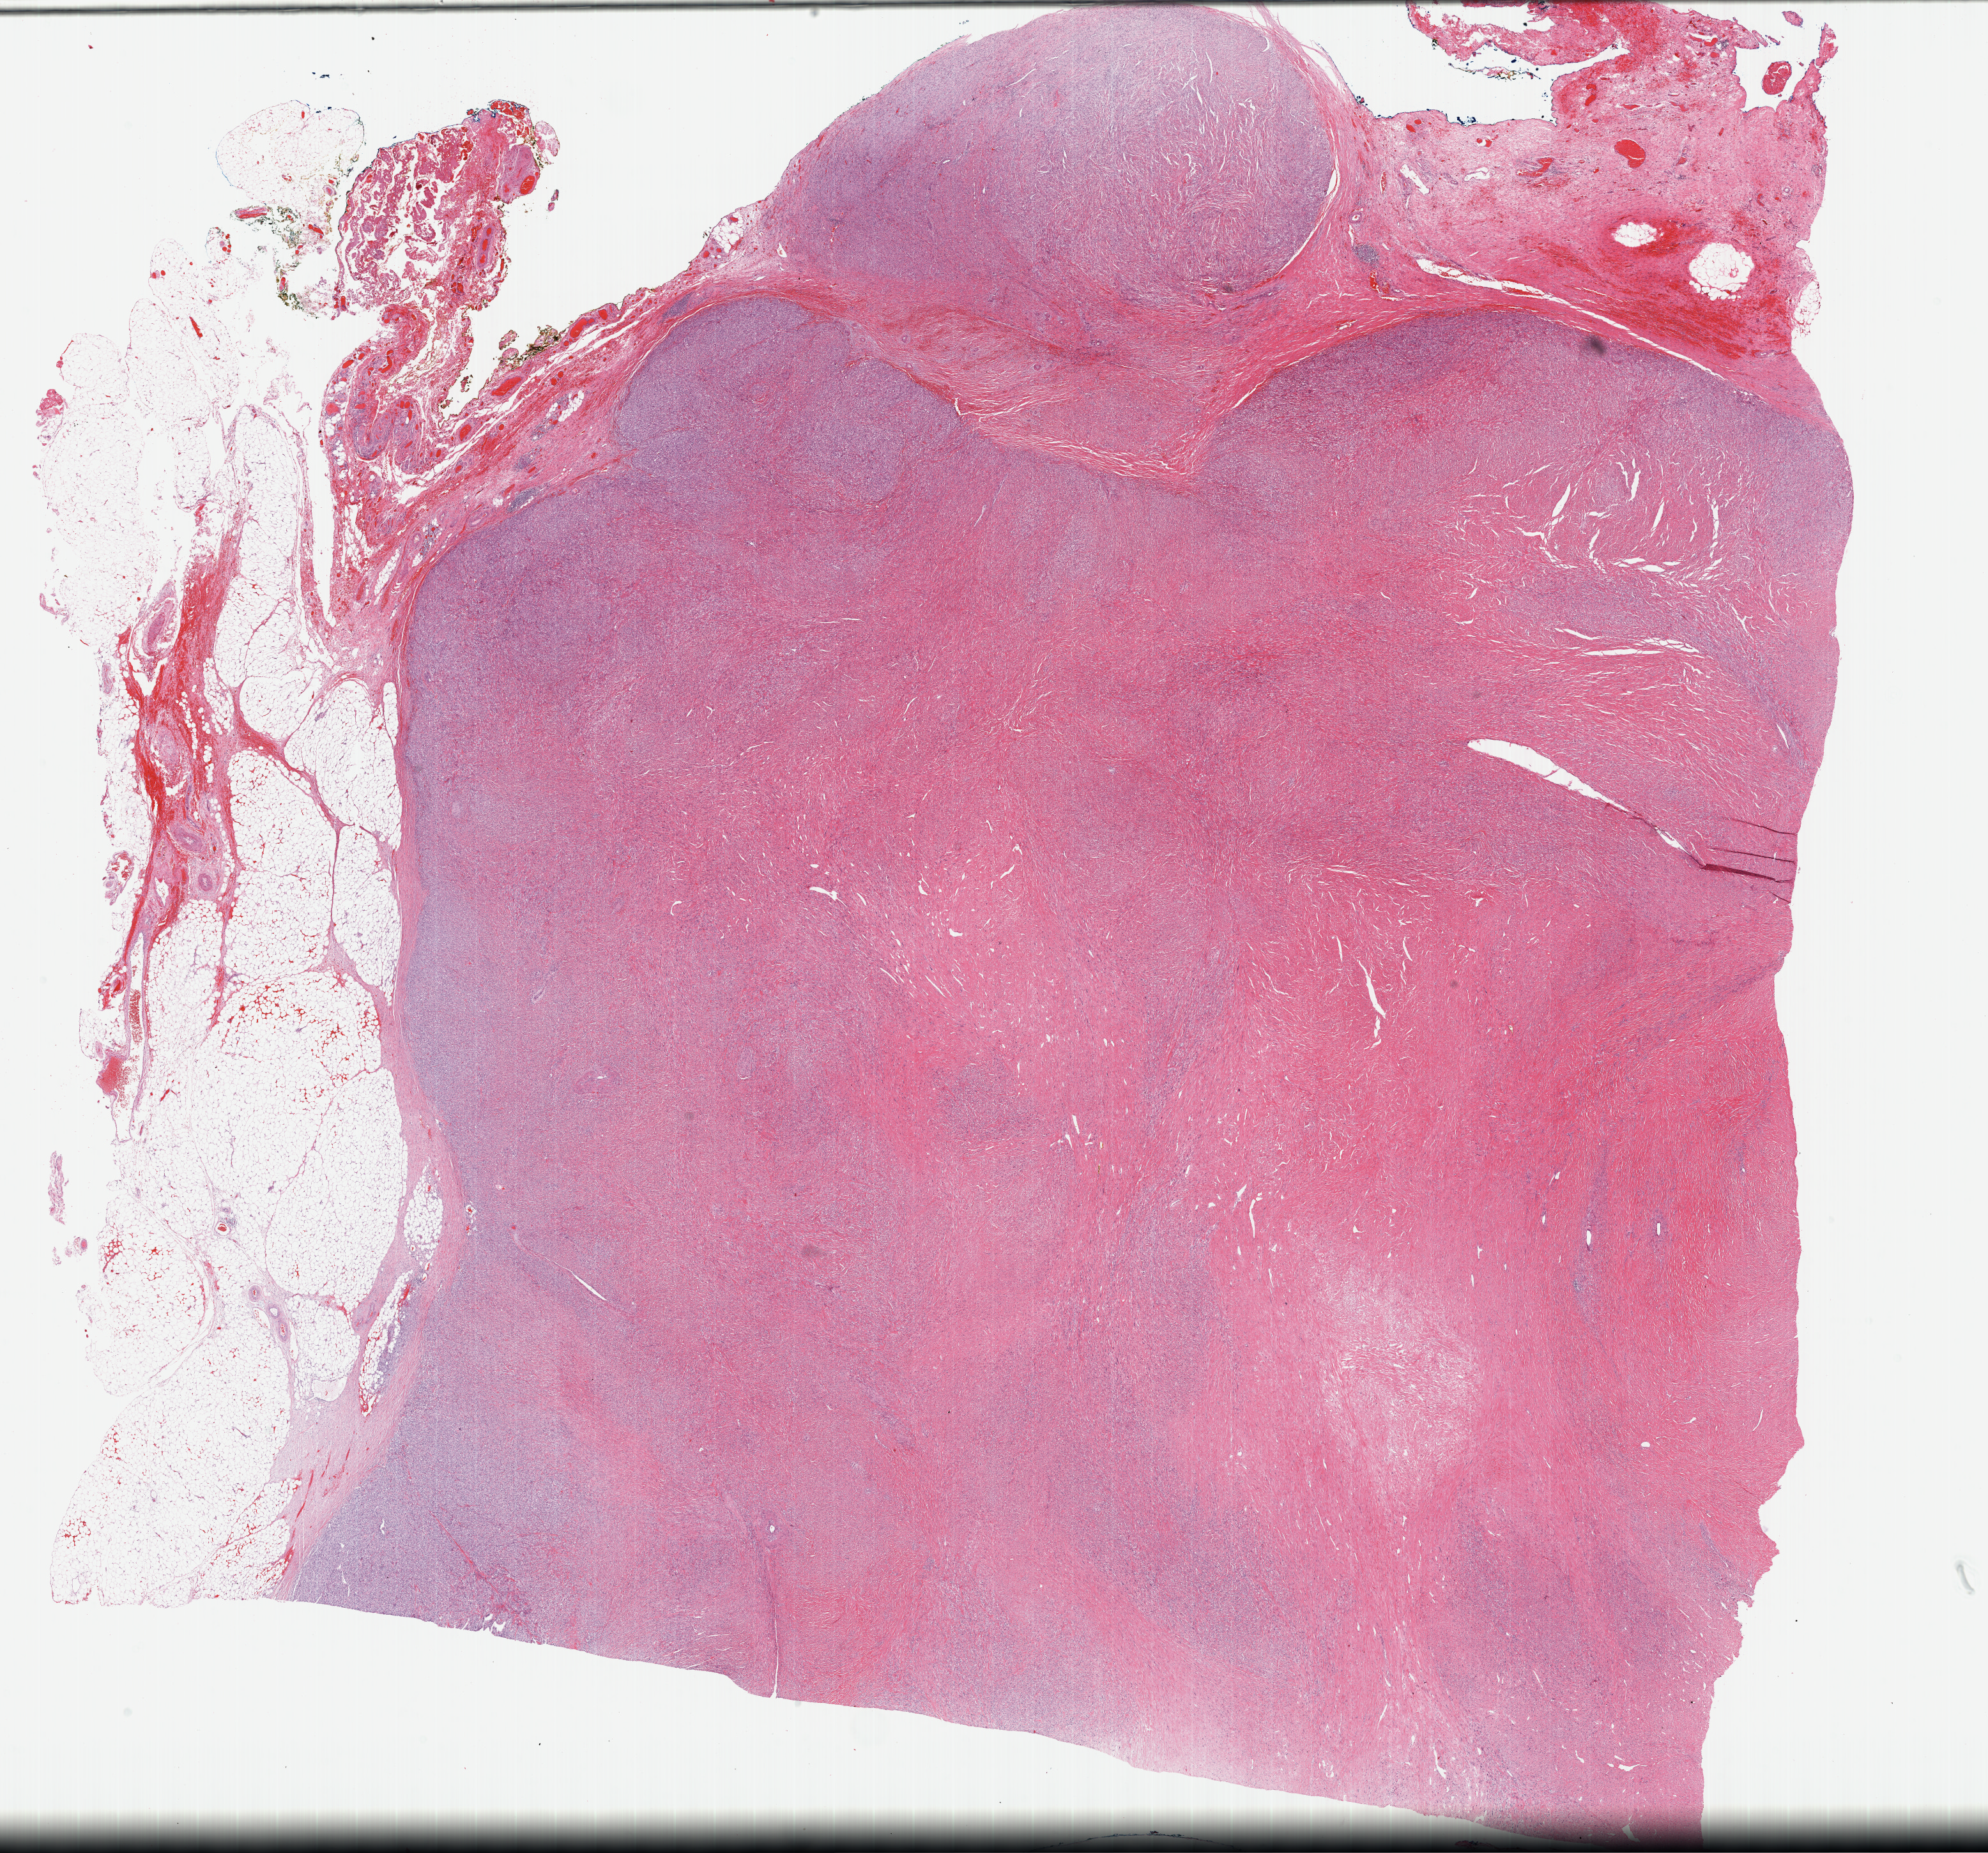
Whole-slide histology image, H&E-stained — shown as a low-resolution overview of the whole scanned area (about 25.2 x 23.5 mm, from a 40x scan); formalin-fixed paraffin-embedded (FFPE) diagnostic section; primary tumour sample from the retroperitoneum and peritoneum. Female, age 66 years at initial diagnosis.
* pathologic diagnosis: Dedifferentiated liposarcoma (retroperitoneum)